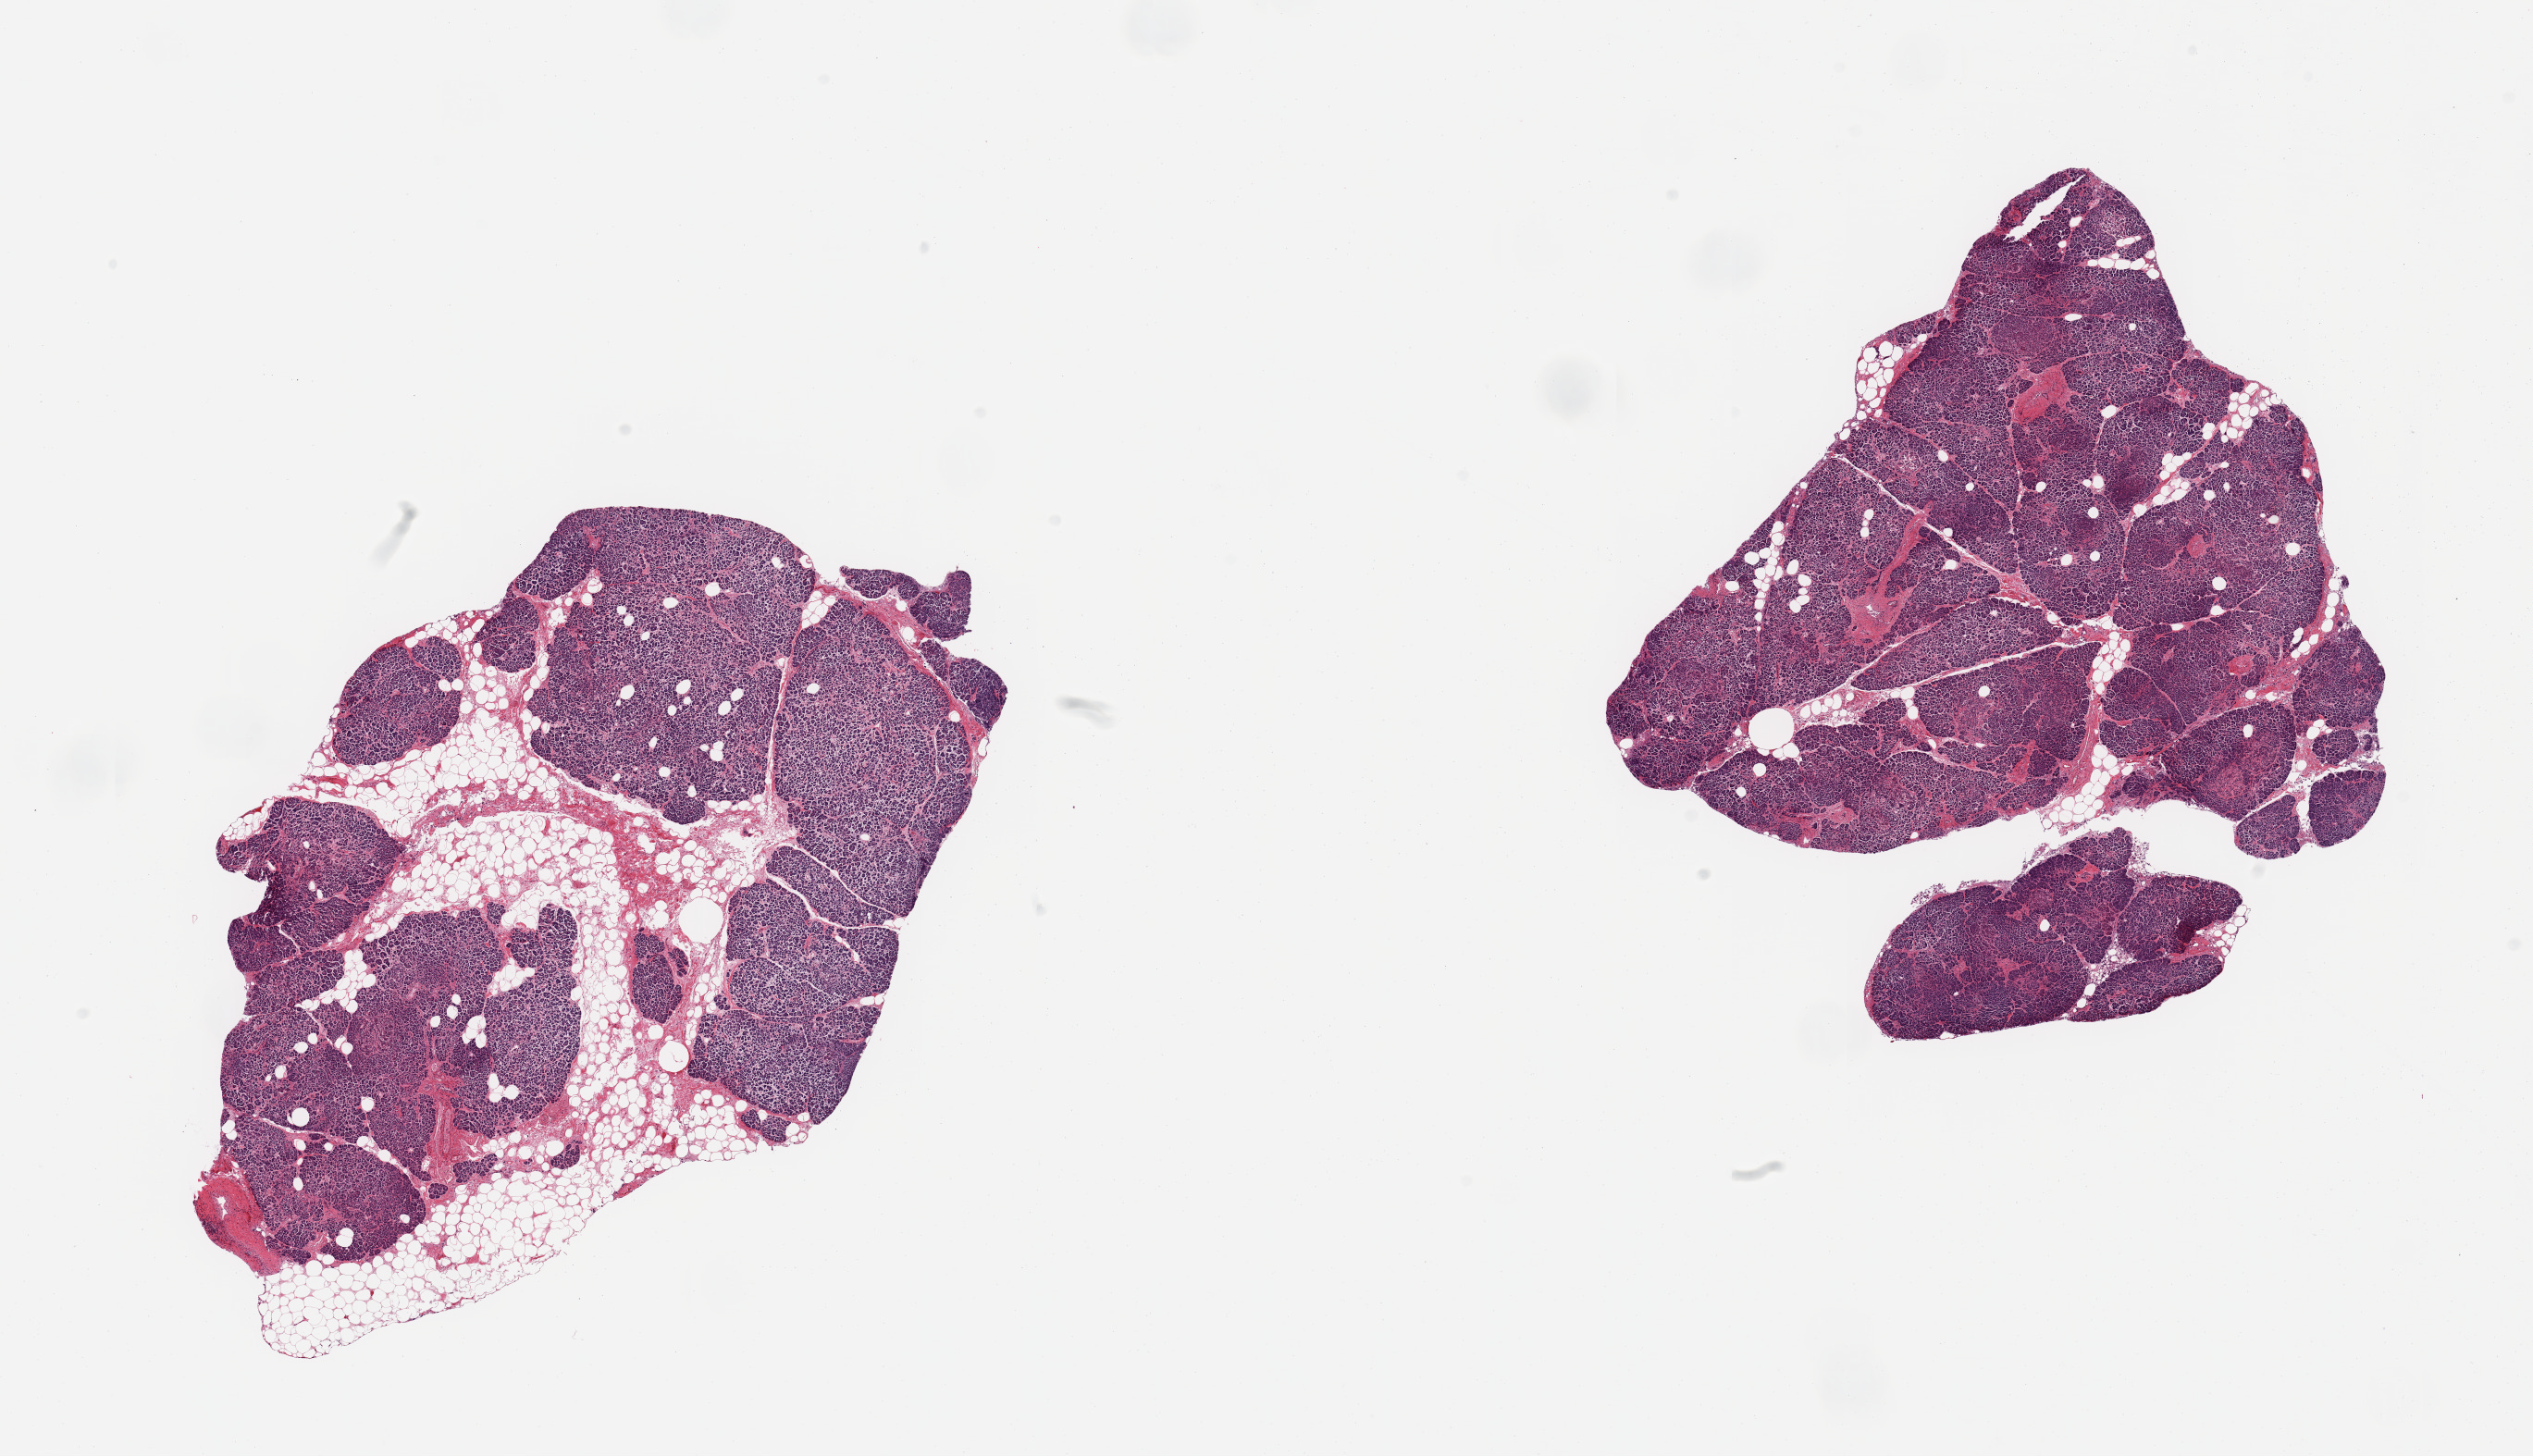
Whole-slide image, H&E stain, whole scanned area (about 21.7 x 12.5 mm) shown as a low-resolution overview, PAXgene-fixed, paraffin-embedded tissue, sampled site (target tissue): pancreas, tissue donor sample. Male donor.
• review note (as recorded): 2 pieces; 30% and 5% internal fat; fairly prominent islets, moderate to severe autolysis